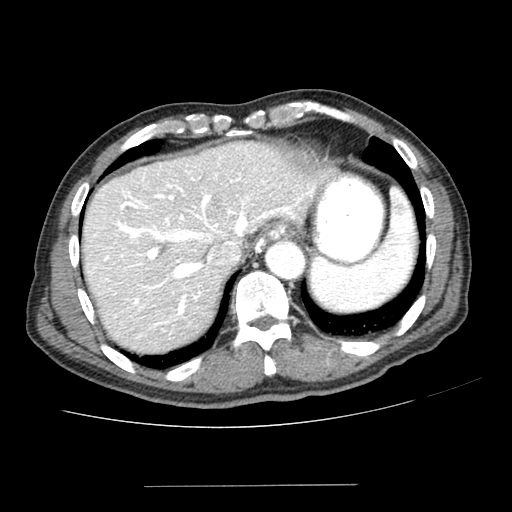
Contrast-enhanced abdominal CT (liver protocol), one axial slice. Position 169 of 187 along the scan axis. Reconstruction kernel SOFT. 100 kVp. One of 2 acquisitions stored at this slice position. Soft-tissue window (W 400 / L 40 HU). 2.5 mm slice thickness. 512 × 512 image matrix, field of view 360 × 360 mm. From the clinical record (not read from this slice): diagnosis: hepatocellular carcinoma (patient treated with transarterial chemoembolisation; whether this scan precedes or follows treatment is not stated here); TNM stage (as recorded): Stage-I; Child-Pugh class: A; tumour differentiation: poorly differentiated; tumour nodularity: uninodular.
Structures marked on this image (semi-automatic segmentation, software-assisted and operator-edited):
- liver parenchyma outside the tumour (the mass and vessels are separate outlines, so this box may not span the whole liver): bounding box (x1, y1, x2, y2) in pixels: (82, 142, 336, 352)
- liver vessels: (93, 164, 315, 338)